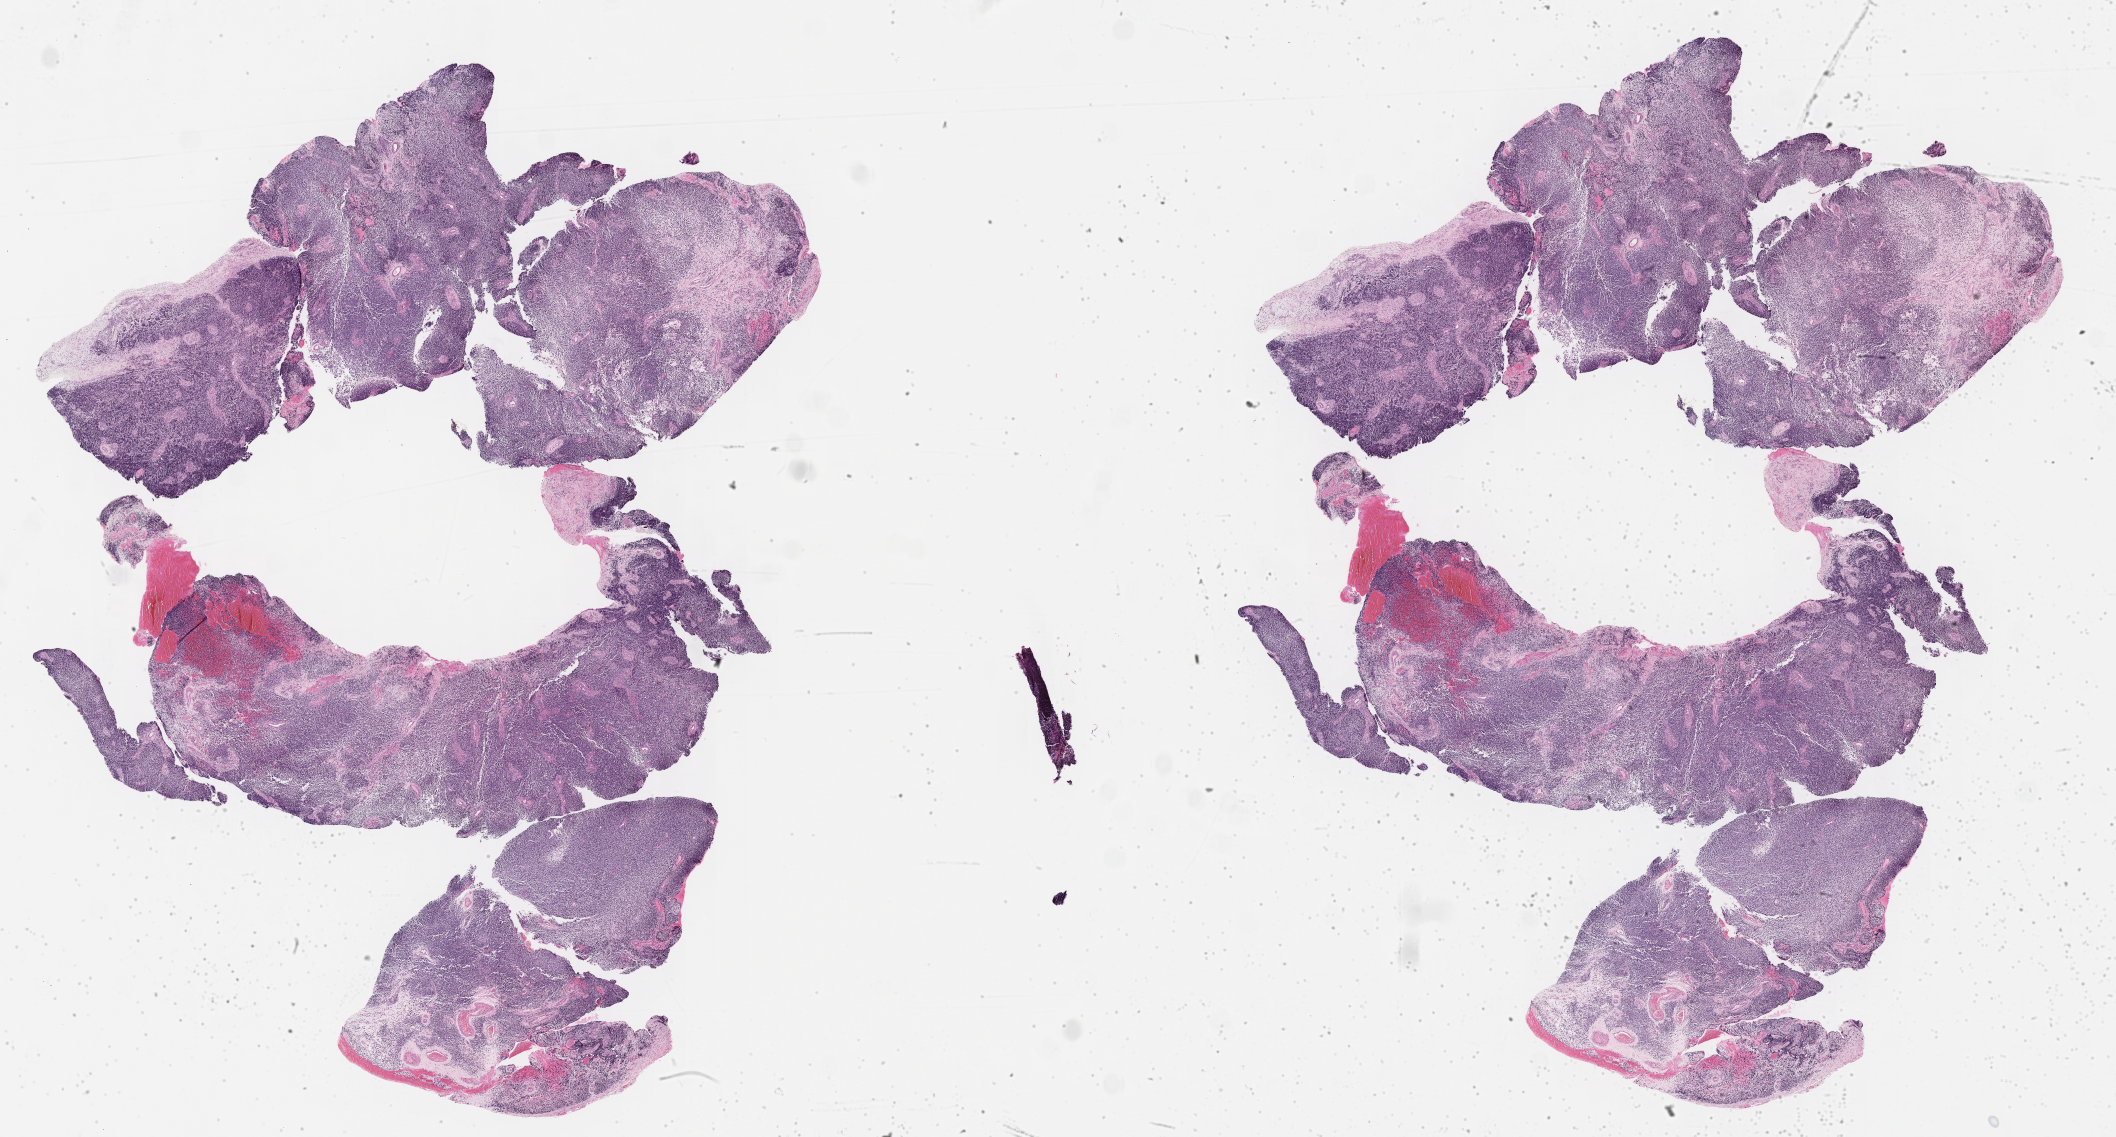
Digitized hematoxylin and eosin (H&E)-stained section of tumor tissue, shown as a low-resolution overview of the whole scanned area (about 34.2 x 18.4 mm). Formalin-fixed paraffin-embedded section. Site: eye - orbit, right. Female patient, age at diagnosis 11.9 years.
Metastatic status at presentation (as recorded): non-metastatic. Diagnosis: rhabdomyosarcoma; histological classification: embryonal rhabdomyosarcoma. Stage (as recorded): 1.